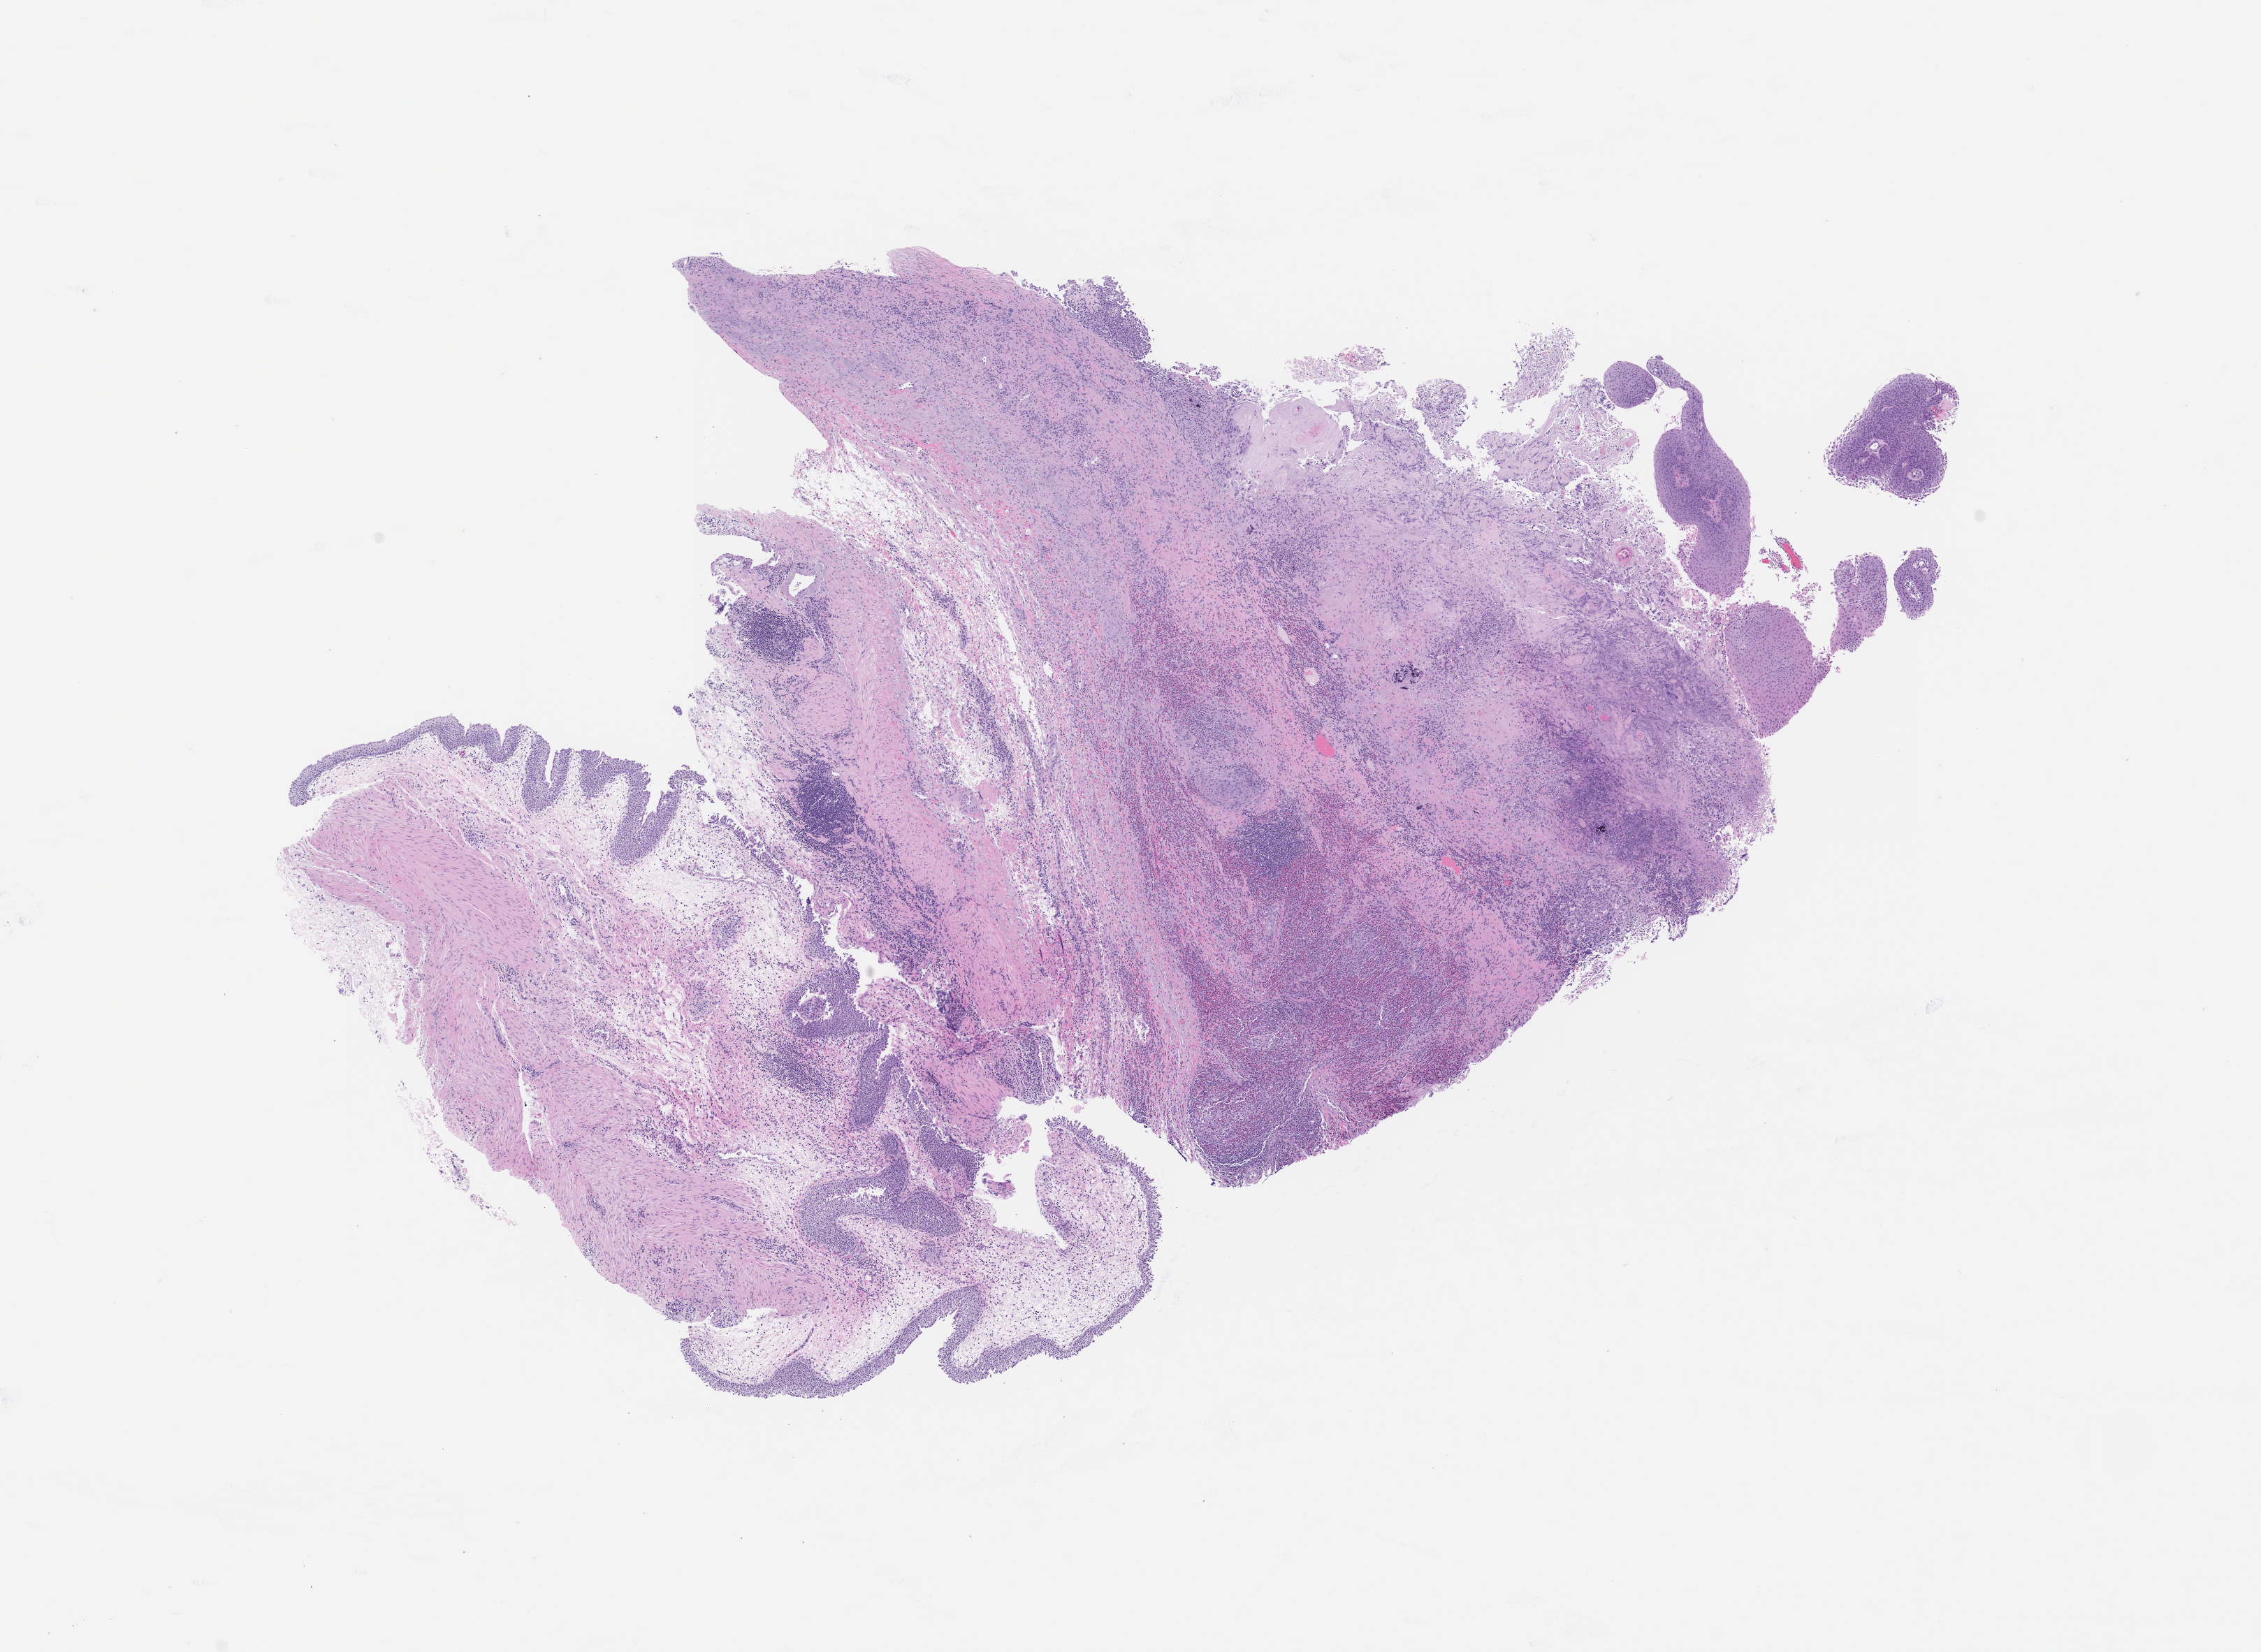
H&E whole-slide image of the patient's (originator) tumor tissue — a low-resolution overview of the entire scanned area, about 13.0 x 9.5 mm; formalin-fixed paraffin-embedded section; tumor site category: bladder. Patient male; aged 50.
• diagnosis: Transitional Cell Carcinoma